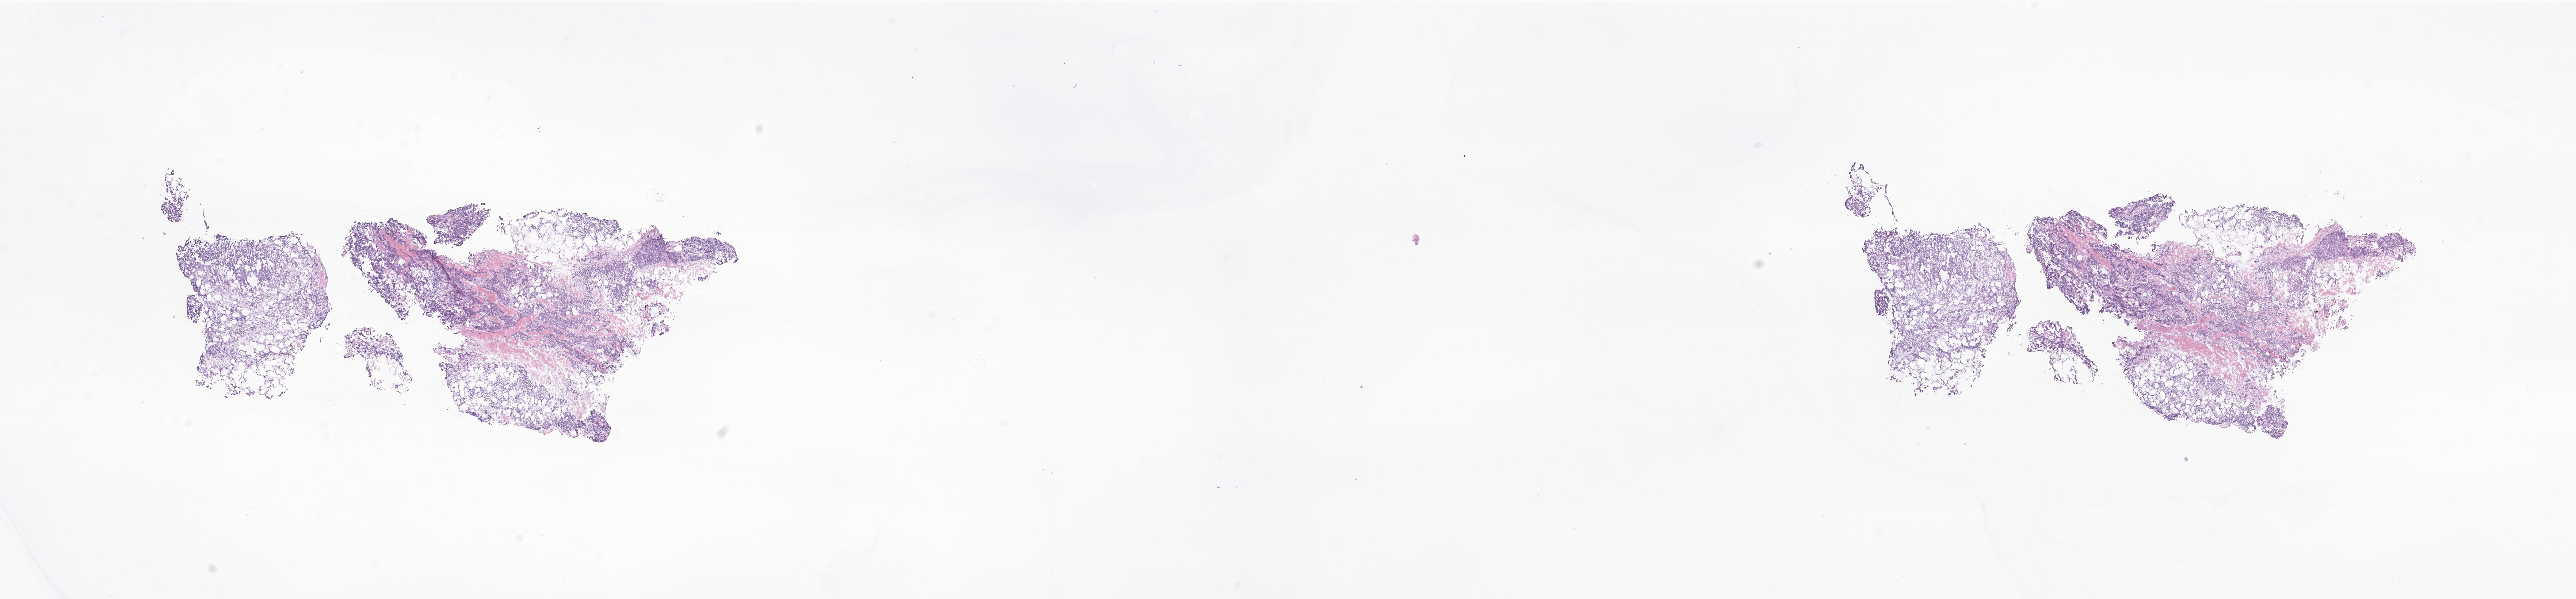
Hematoxylin and eosin (H&E) whole-slide image of tumor tissue from the soft tissue of upper extremity, whole scanned area (about 29.7 x 6.9 mm) shown as a low-resolution overview. Frozen section. Patient: male, age 177 months (14 years 9 months).
Recorded diagnosis: Embryonal rhabdomyosarcoma, NOS. Tissue or organ of origin (case record): connective, subcutaneous and other soft tissues of upper limb and shoulder.